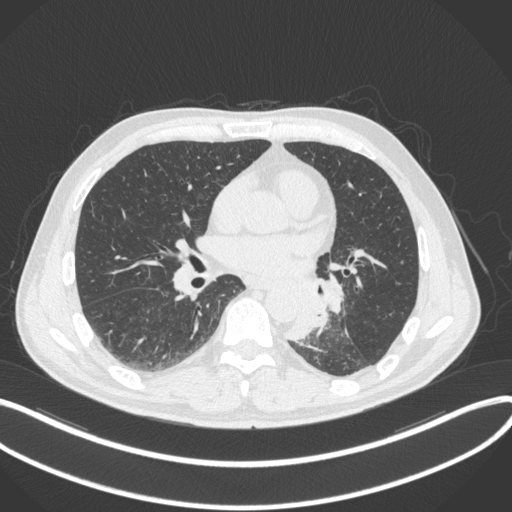
Chest CT, one axial slice; position 158 of 328 along the scan axis; reconstruction kernel B31f; lung window (W 1500 / L -600 HU); 512 × 512 image matrix. Patient: male, 59 years. From the clinical record (not read from this slice): clinical TNM (as recorded): T2a N2 M0.
Structures marked on this image (rectangle marked by the reading radiologist):
- lung tumour (recorded histology: squamous cell carcinoma): bounding box <283,276,339,342> (left, top, right, bottom; pixels)